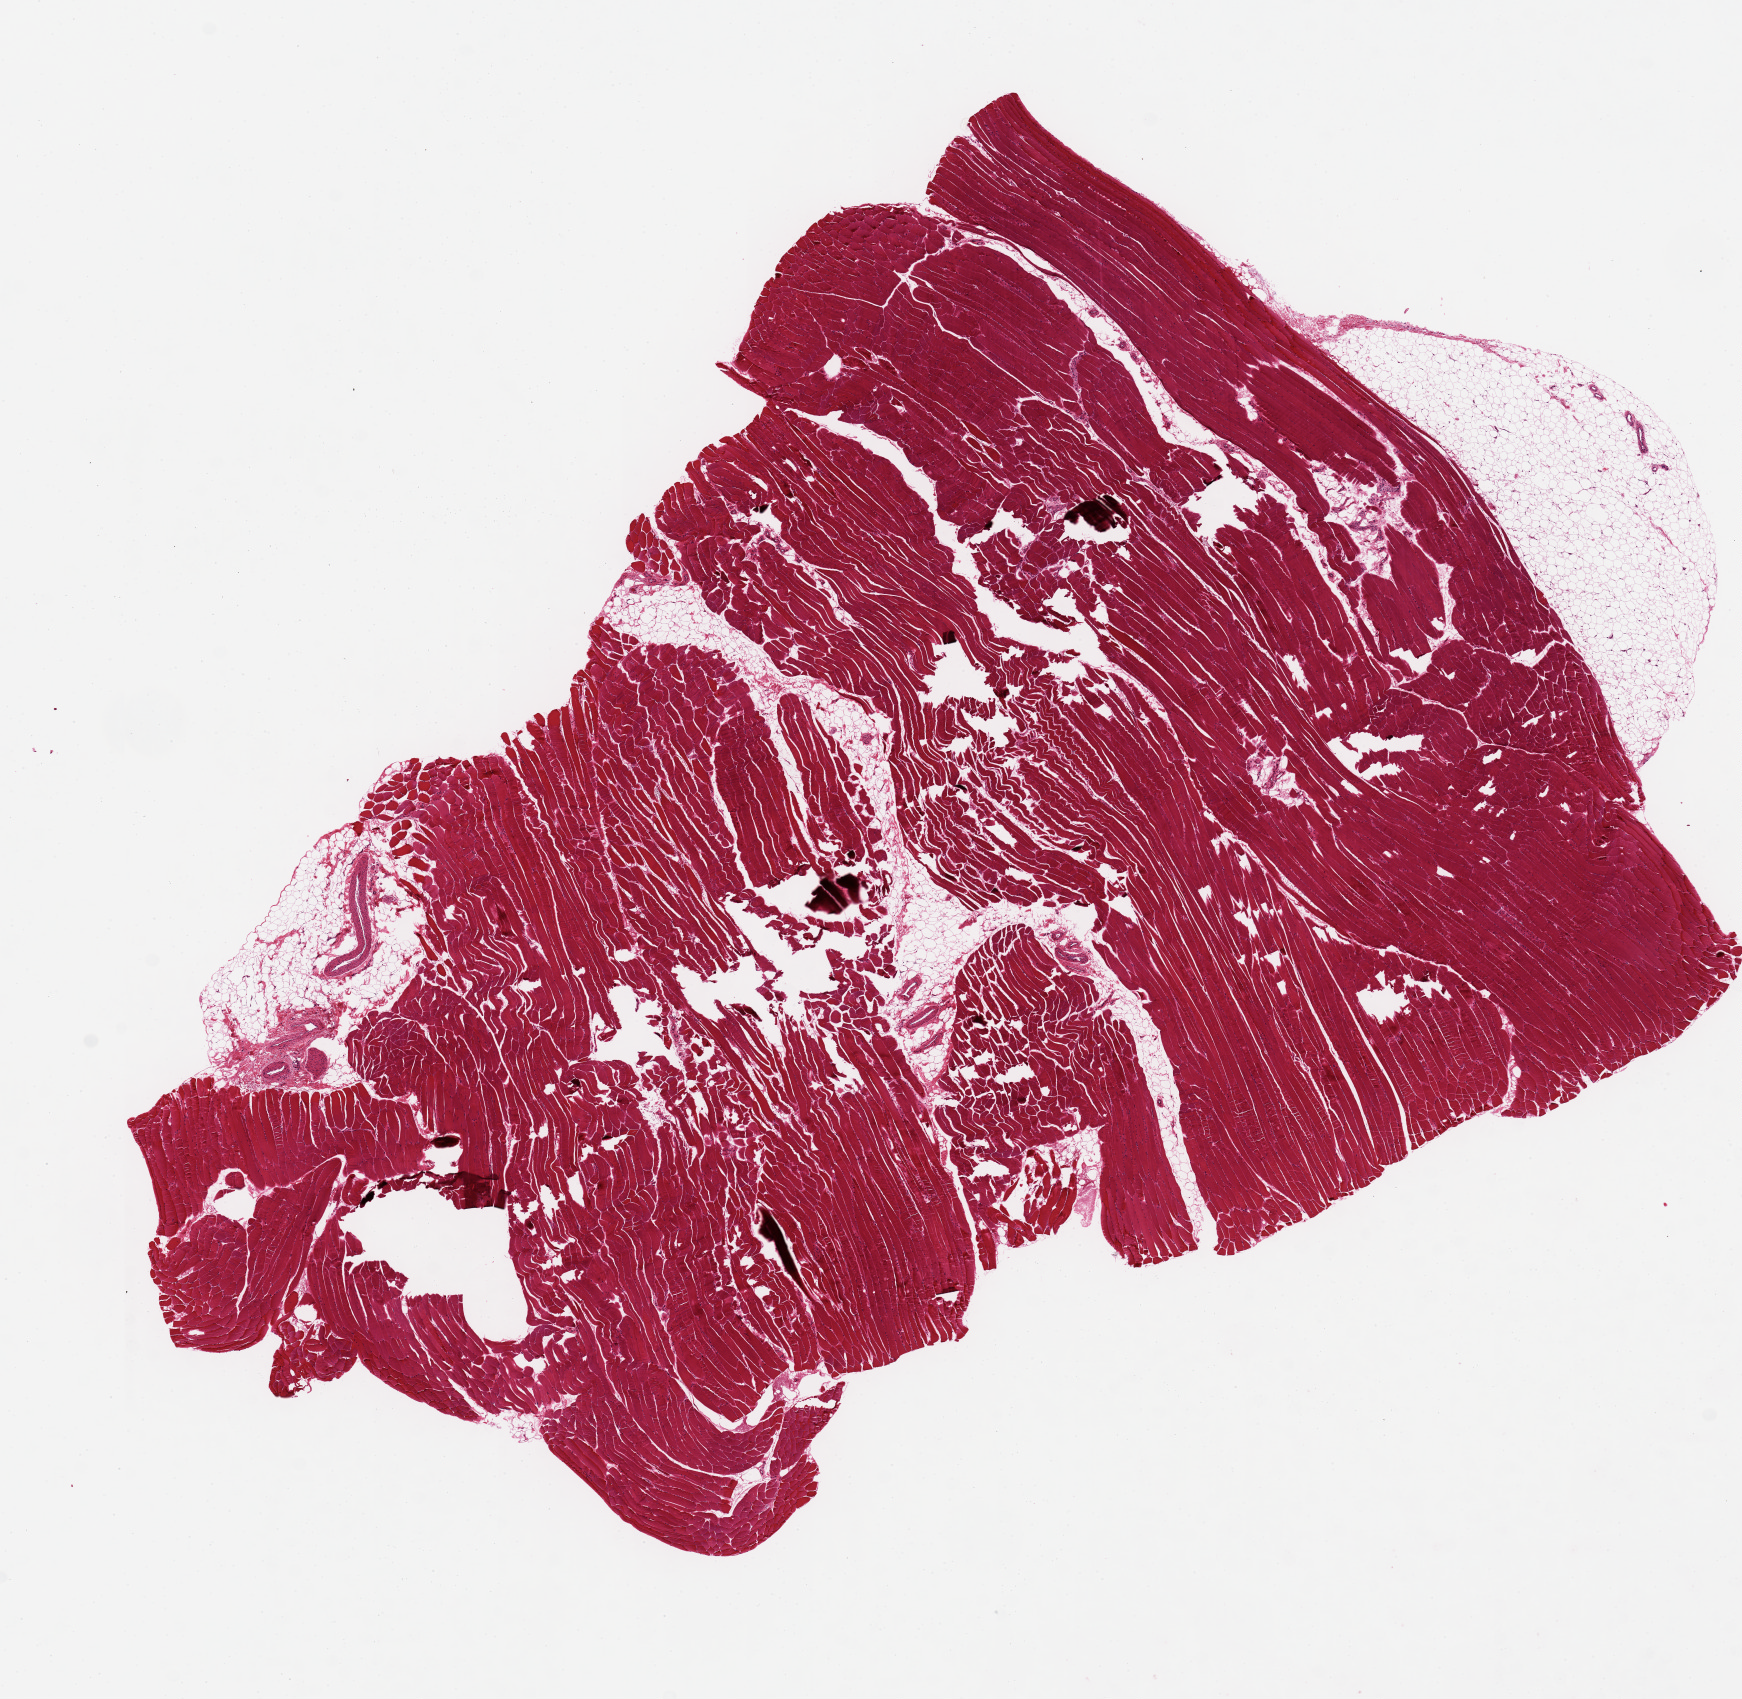
Digitized hematoxylin and eosin (H&E)-stained section, brightfield — shown as a low-resolution overview of the whole scanned area (about 13.8 x 13.4 mm); PAXgene-fixed paraffin-embedded (PFPE) section; section of skeletal muscle (target tissue); donor tissue sample. Donor sex: male.
- pathologist's review note for this sample: Severe tissue fracture, probably fixation artifact. Plenty of good muscle otherwise. 12x9mm. 10% fat at edges